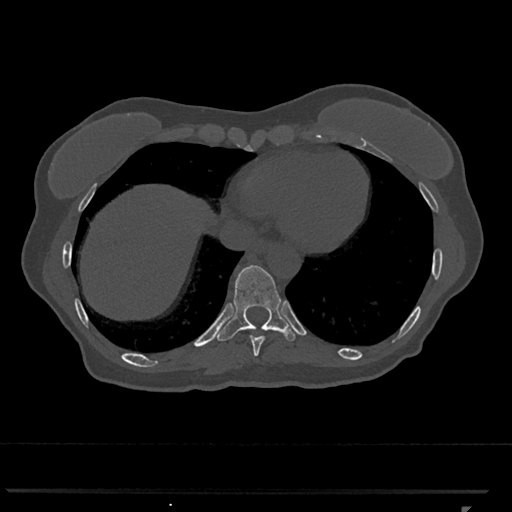
CT including the spine, one axial slice; slice 585 of 793 in the series (ordered by position); reconstruction kernel Br40s/3; bone window (W 1800 / L 400 HU); 0.5 mm slice thickness; 512 × 512 image matrix, field of view 380 × 380 mm. Female patient, age 62 years. From the clinical record (not read from this slice): primary cancer: renal.
Outlined on this slice (semi-automatically segmented with operator editing):
- T10 vertebra: bounding box (x1, y1, x2, y2) in pixels: (217, 265, 297, 341)
- T9 vertebra: (250, 336, 265, 357)